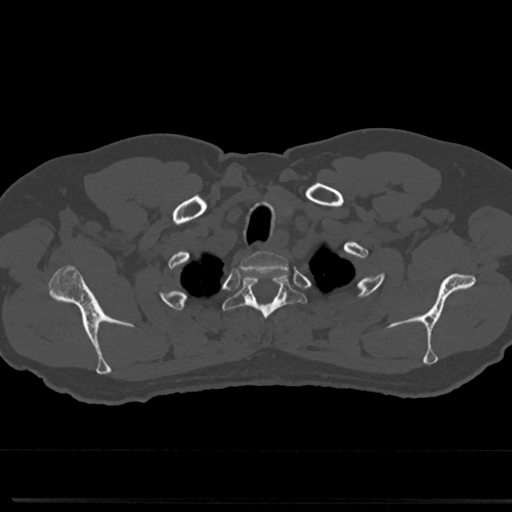
CT including the spine, one axial slice; position 644 of 817 along the scan axis; 120 kVp; bone window (W 1800 / L 400 HU); 512 × 512 image matrix, field of view 355 × 355 mm. Patient: male, 61 years. Case-level facts recorded for this patient, not image findings: primary cancer: prostate.
Structures marked on this image (semi-automatic segmentation, software-assisted and operator-edited):
- T1 vertebra: box from (x=244, y=252) to (x=285, y=265) px
- T2 vertebra: (x=227, y=272)–(x=302, y=347)